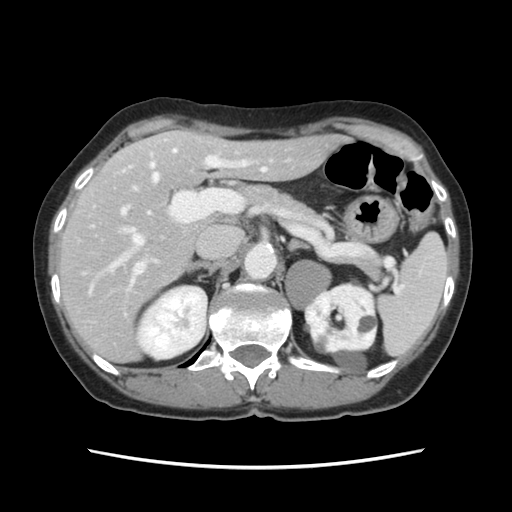
Contrast-enhanced abdominal CT, one axial slice. Position 78 of 120 along the scan axis. 120 kVp. Intravenous contrast given. Soft-tissue window (W 400 / L 40 HU). 2.5 mm slice thickness. 512 × 512 image matrix. Female patient, age 70 years. From the clinical record (not read from this slice): diagnosis: colorectal cancer liver metastases, imaged before liver resection; multiple liver metastases: no.
Structures marked on this image (outlined manually by an expert reader):
- hepatic veins: bounding box <109,149,176,270> (left, top, right, bottom; pixels)
- liver: <60,132,339,361>
- planned liver remnant (the part of the liver to remain after resection): <94,131,341,285>
- portal vein (with intrahepatic branches): <121,140,247,288>